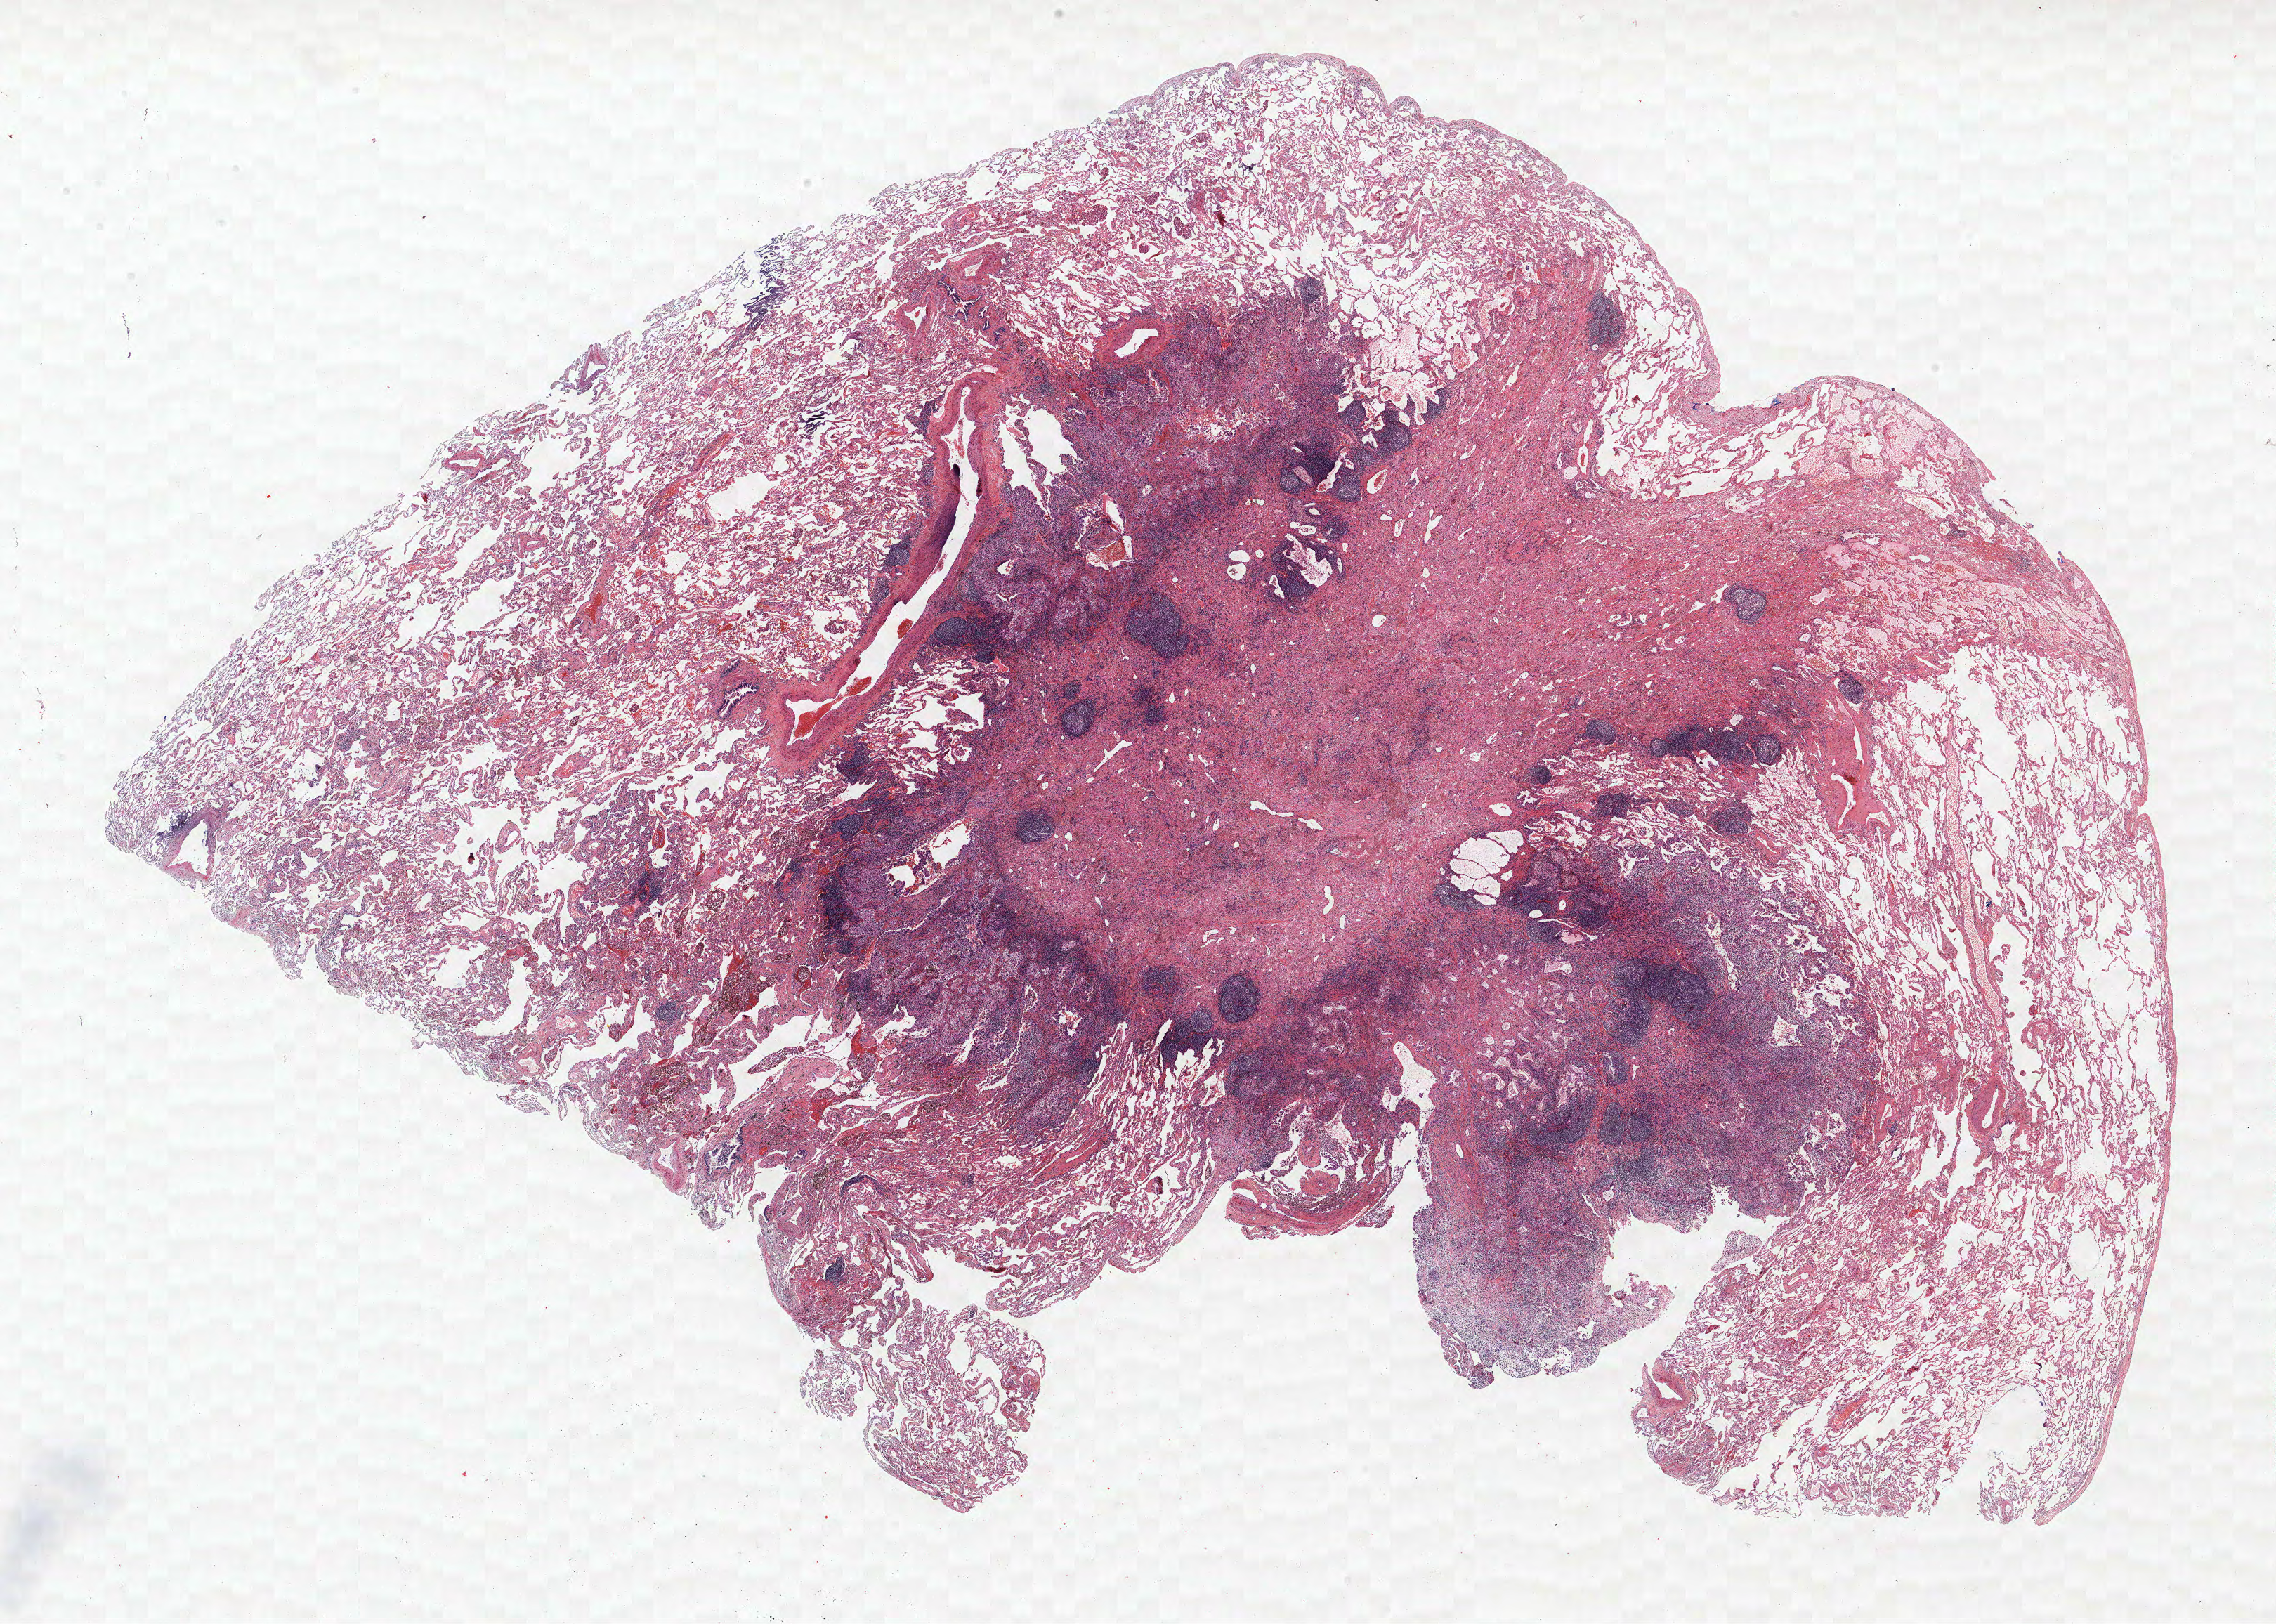
Whole-slide histology image, H&E-stained — whole scanned area (about 25.9 x 18.5 mm) shown as a low-resolution overview. Formalin-fixed paraffin-embedded (FFPE) section. Lung tissue. Female, age 65 at enrolment. Current smoker at enrolment. Grade: moderately differentiated (G2).
• participant's lung-cancer diagnosis: Acinar cell carcinoma (ICD-O-3 8550/3)
• stage (AJCC 6th edition): IA
• tumour size (pathology): 15 mm
• primary tumour location (clinical record): right upper lobe